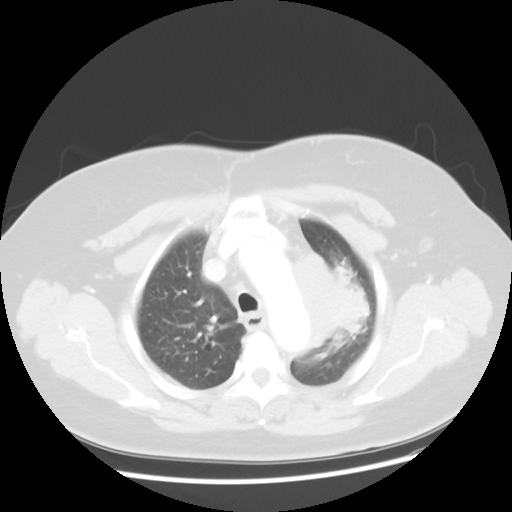
Chest CT, one axial slice. Position 37 of 49 along the scan axis. Reconstruction kernel STANDARD. 120 kVp. Lung window (W 1500 / L -600 HU). 5 mm slice thickness. 512 × 512 image matrix, field of view 374 × 374 mm. Patient: female, 58 years. Case-level facts recorded for this patient, not image findings: clinical TNM (as recorded): T4 N3 M0.
Outlined on this slice (rectangle marked by the reading radiologist):
- lung tumour (recorded histology: small cell carcinoma): bounding box (x1, y1, x2, y2) in pixels: (292, 250, 376, 349)